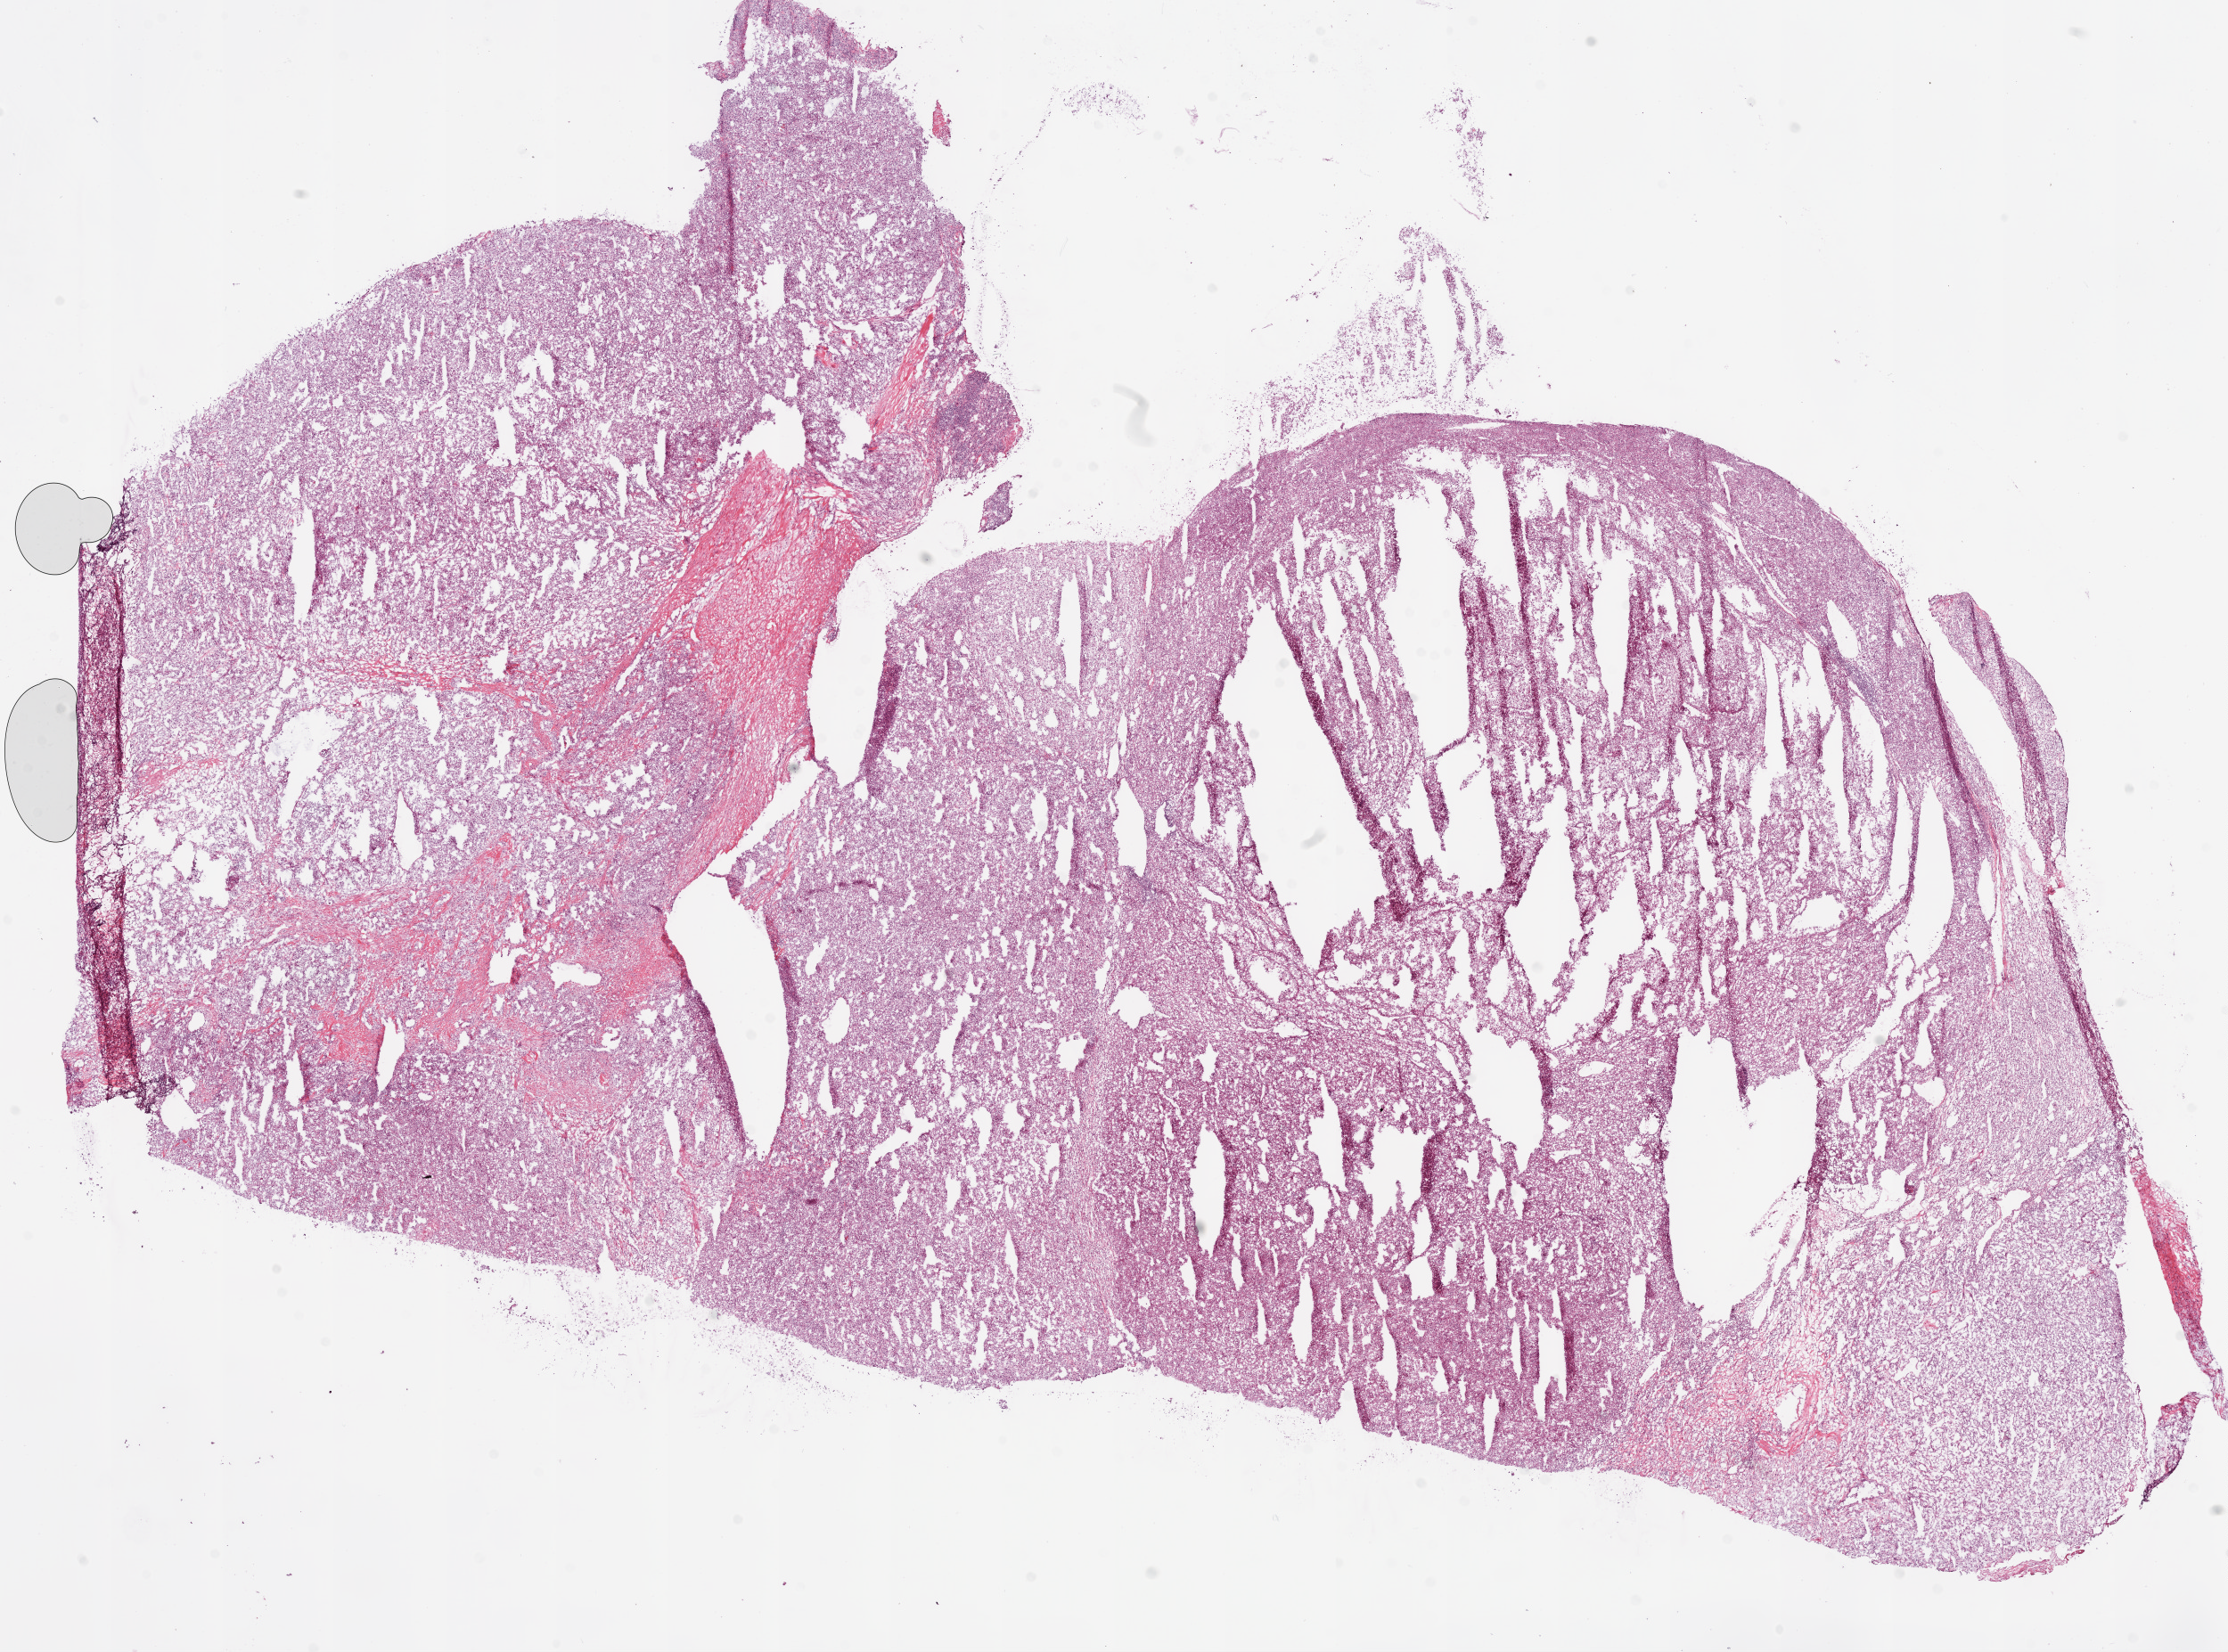
H&E-stained whole-slide image, a low-resolution overview of the entire scanned area, about 20.1 x 14.9 mm (slide scanned at 20x). Frozen section from the bottom of the tissue portion. Sample: primary tumour, kidney. Female patient; age at initial diagnosis 53 years. Histologic grade: G3 (poorly differentiated). Composition of this section per pathologist review: tumour cells 90%, tumour nuclei 85%, normal cells 0%, stromal cells 10%, necrosis 0%.
AJCC pathologic stage: IV. Diagnosis: Clear cell adenocarcinoma, NOS.